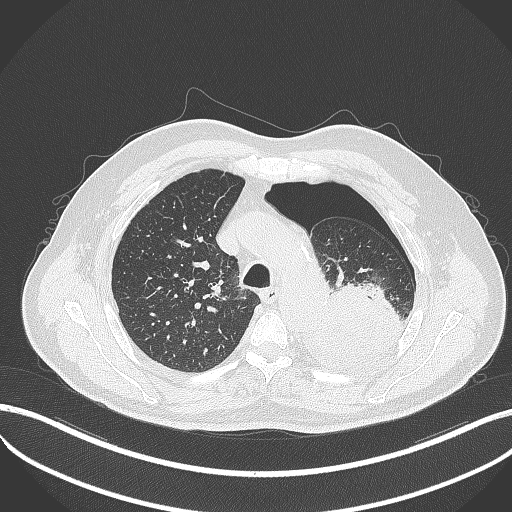
Chest CT, one axial slice; position 379 of 464 along the scan axis; reconstruction kernel B70f; 120 kVp; lung window (W 1500 / L -600 HU); 1 mm slice thickness; 512 × 512 image matrix, field of view 400 × 400 mm. Male patient, age 76 years. Case-level facts recorded for this patient, not image findings: clinical TNM (as recorded): T3 N0 M1b.
Structures marked on this image (rectangle marked by the reading radiologist):
- lung tumour (recorded histology: adenocarcinoma): bounding box <301,279,408,372> (left, top, right, bottom; pixels)